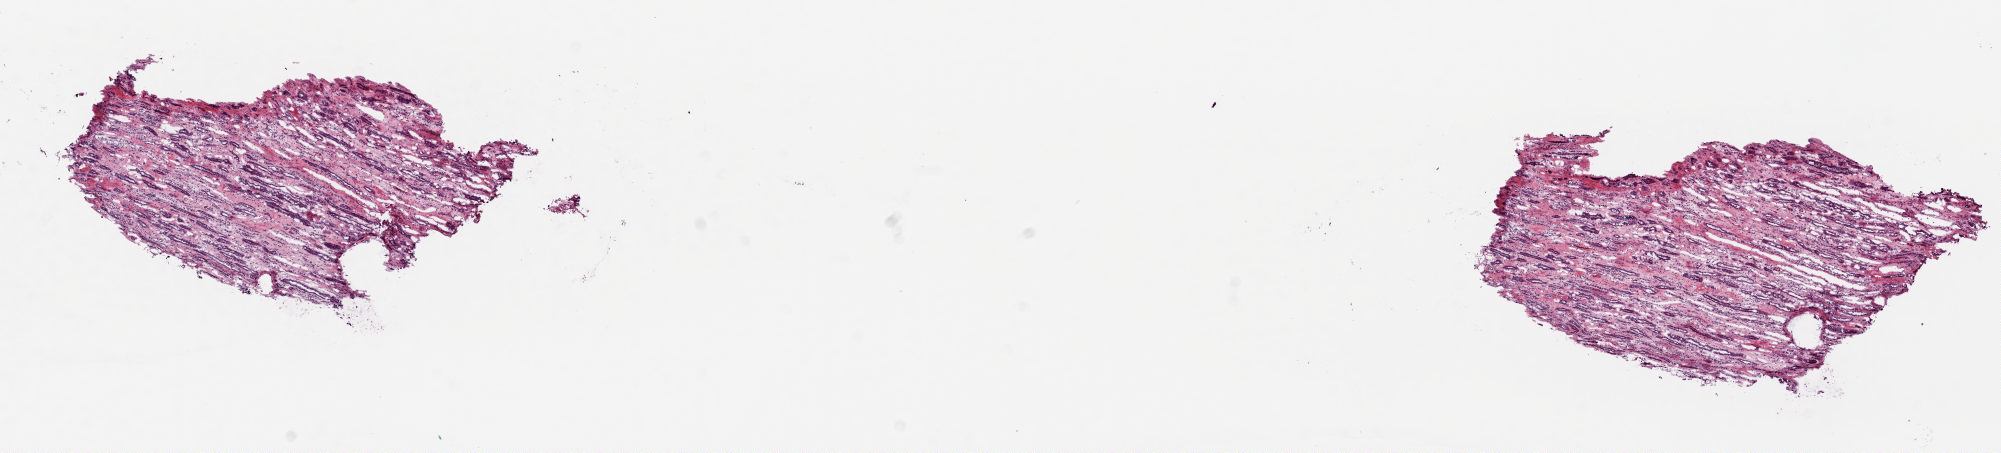
Hematoxylin and eosin (H&E) stained whole-slide image, a low-resolution overview of the entire scanned area, about 15.9 x 3.6 mm. Frozen section from the top of the tissue portion. Kidney, solid tissue normal (non-tumour tissue) sample. Patient: female, age at initial diagnosis 71 years. Pathologist review of this section (percent, as recorded): tumour cells 0%, tumour nuclei 0%, normal cells 100%, stromal cells 0%, necrosis 0%. Inflammatory infiltration, as recorded: lymphocyte infiltration 0%, monocyte infiltration 0%, neutrophil infiltration 0%.
This section: solid tissue normal sample (biorepository sample class). Patient diagnosis: Papillary adenocarcinoma, NOS.